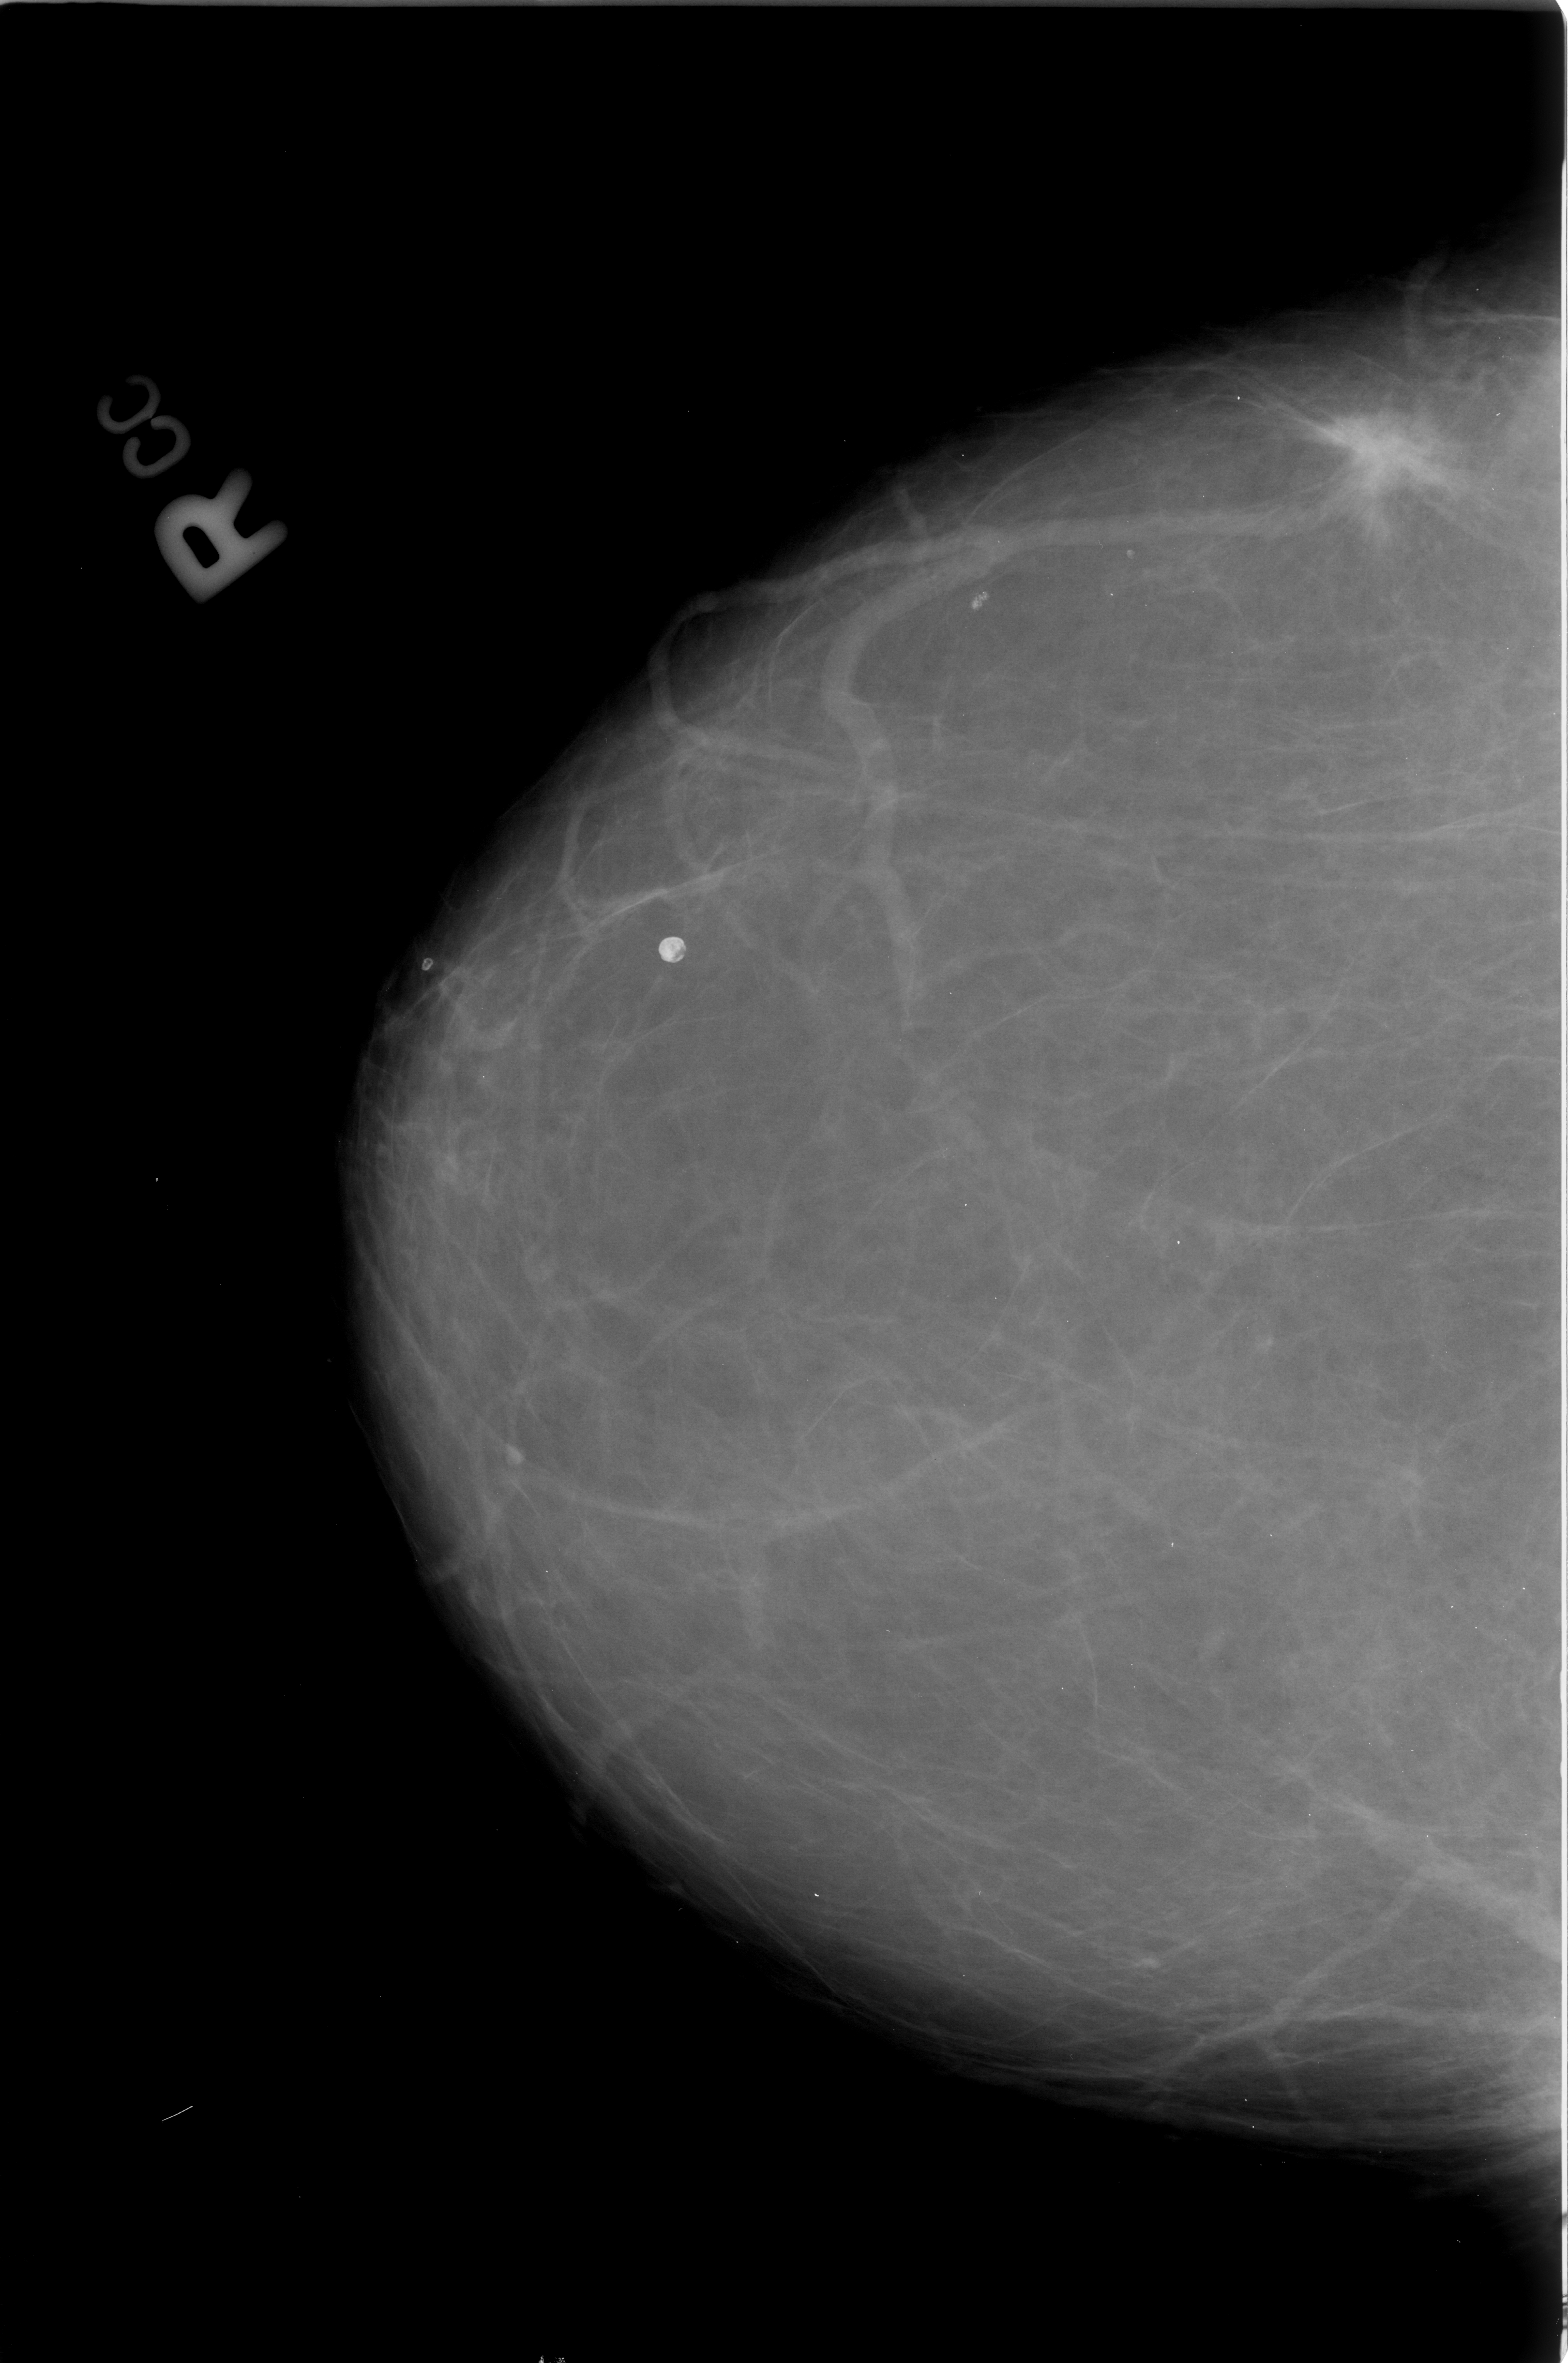
Scanned film-screen mammogram; right breast; CC view; breast composition: almost entirely fatty (BI-RADS density category 1 of 4); 1568 × 2363 image matrix.
Expert-marked regions of interest on this image (one box per marked abnormality):
- mass, shape irregular / architectural distortion, margins spiculated; BI-RADS assessment category 5; subtlety rating 5 on a 1 (subtle) to 5 (obvious) scale; pathology result (as recorded, not read from the image): malignant: bounding box <1317,403,1456,532> (left, top, right, bottom; pixels)